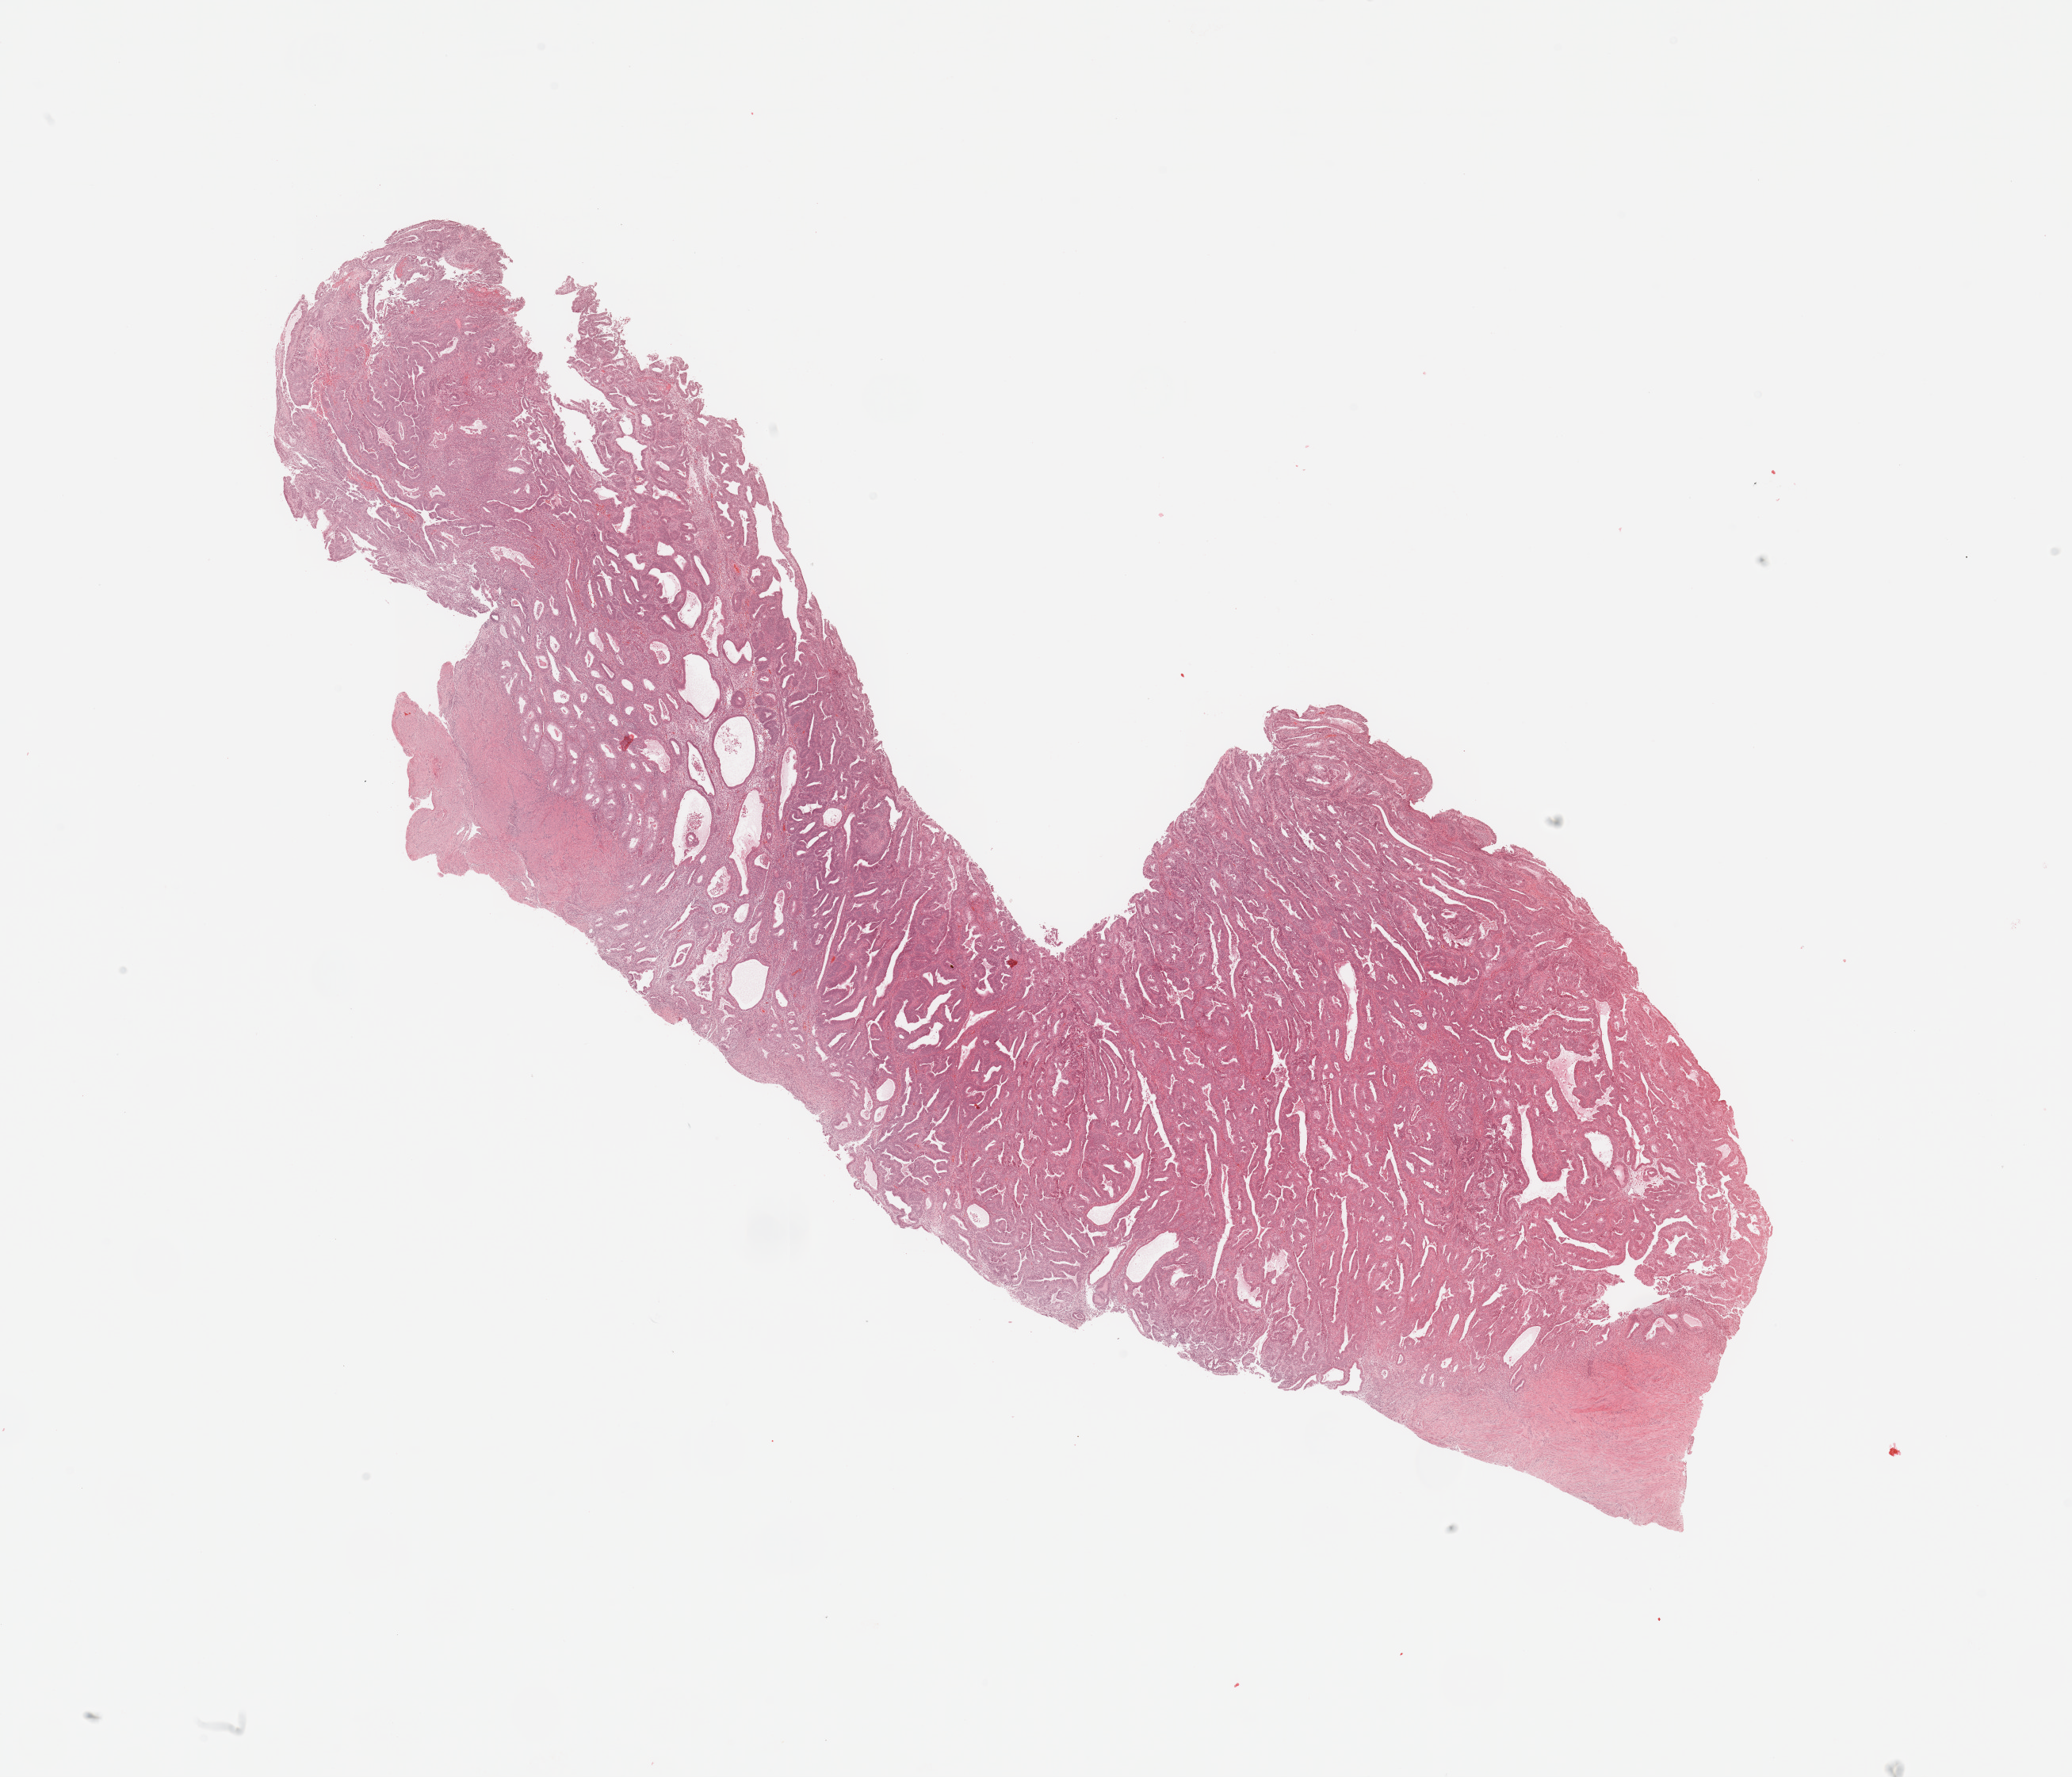
H&E whole-slide image, a low-resolution overview of the entire scanned area, about 20.7 x 17.7 mm; tumour tissue sample, sampled site: uterus. Patient: female, age 56 years. Histologic grade: G2 (moderately differentiated). Composition of this section per pathologist review: tumour nuclei 80%, necrosis 2%.
• histologic diagnosis: Endometrioid adenocarcinoma, NOS
• AJCC pathologic stage: I
• primary tumour site (as recorded): anterior endometrium